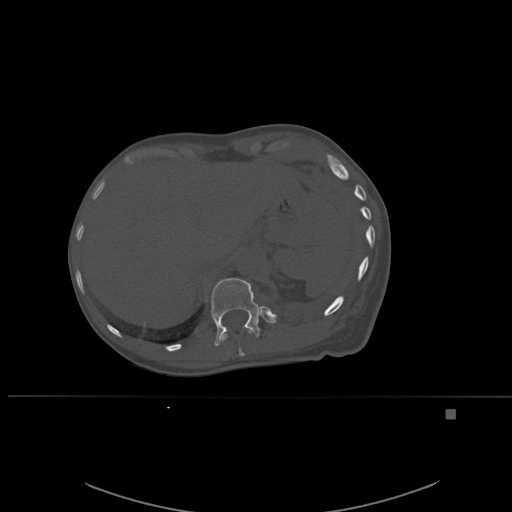
CT including the spine, one axial slice. Slice 286 of 537 in the series (ordered by position). Bone window (W 1800 / L 400 HU). 512 × 512 image matrix, field of view 440 × 440 mm. Female patient, age 45 years. Case-level facts recorded for this patient, not image findings: primary cancer: lung.
Annotated regions visible in this slice (semi-automatically segmented with operator editing):
- T11 vertebra: bounding box [x1, y1, x2, y2] px = [220, 329, 253, 356]
- T12 vertebra: [211, 278, 261, 346]